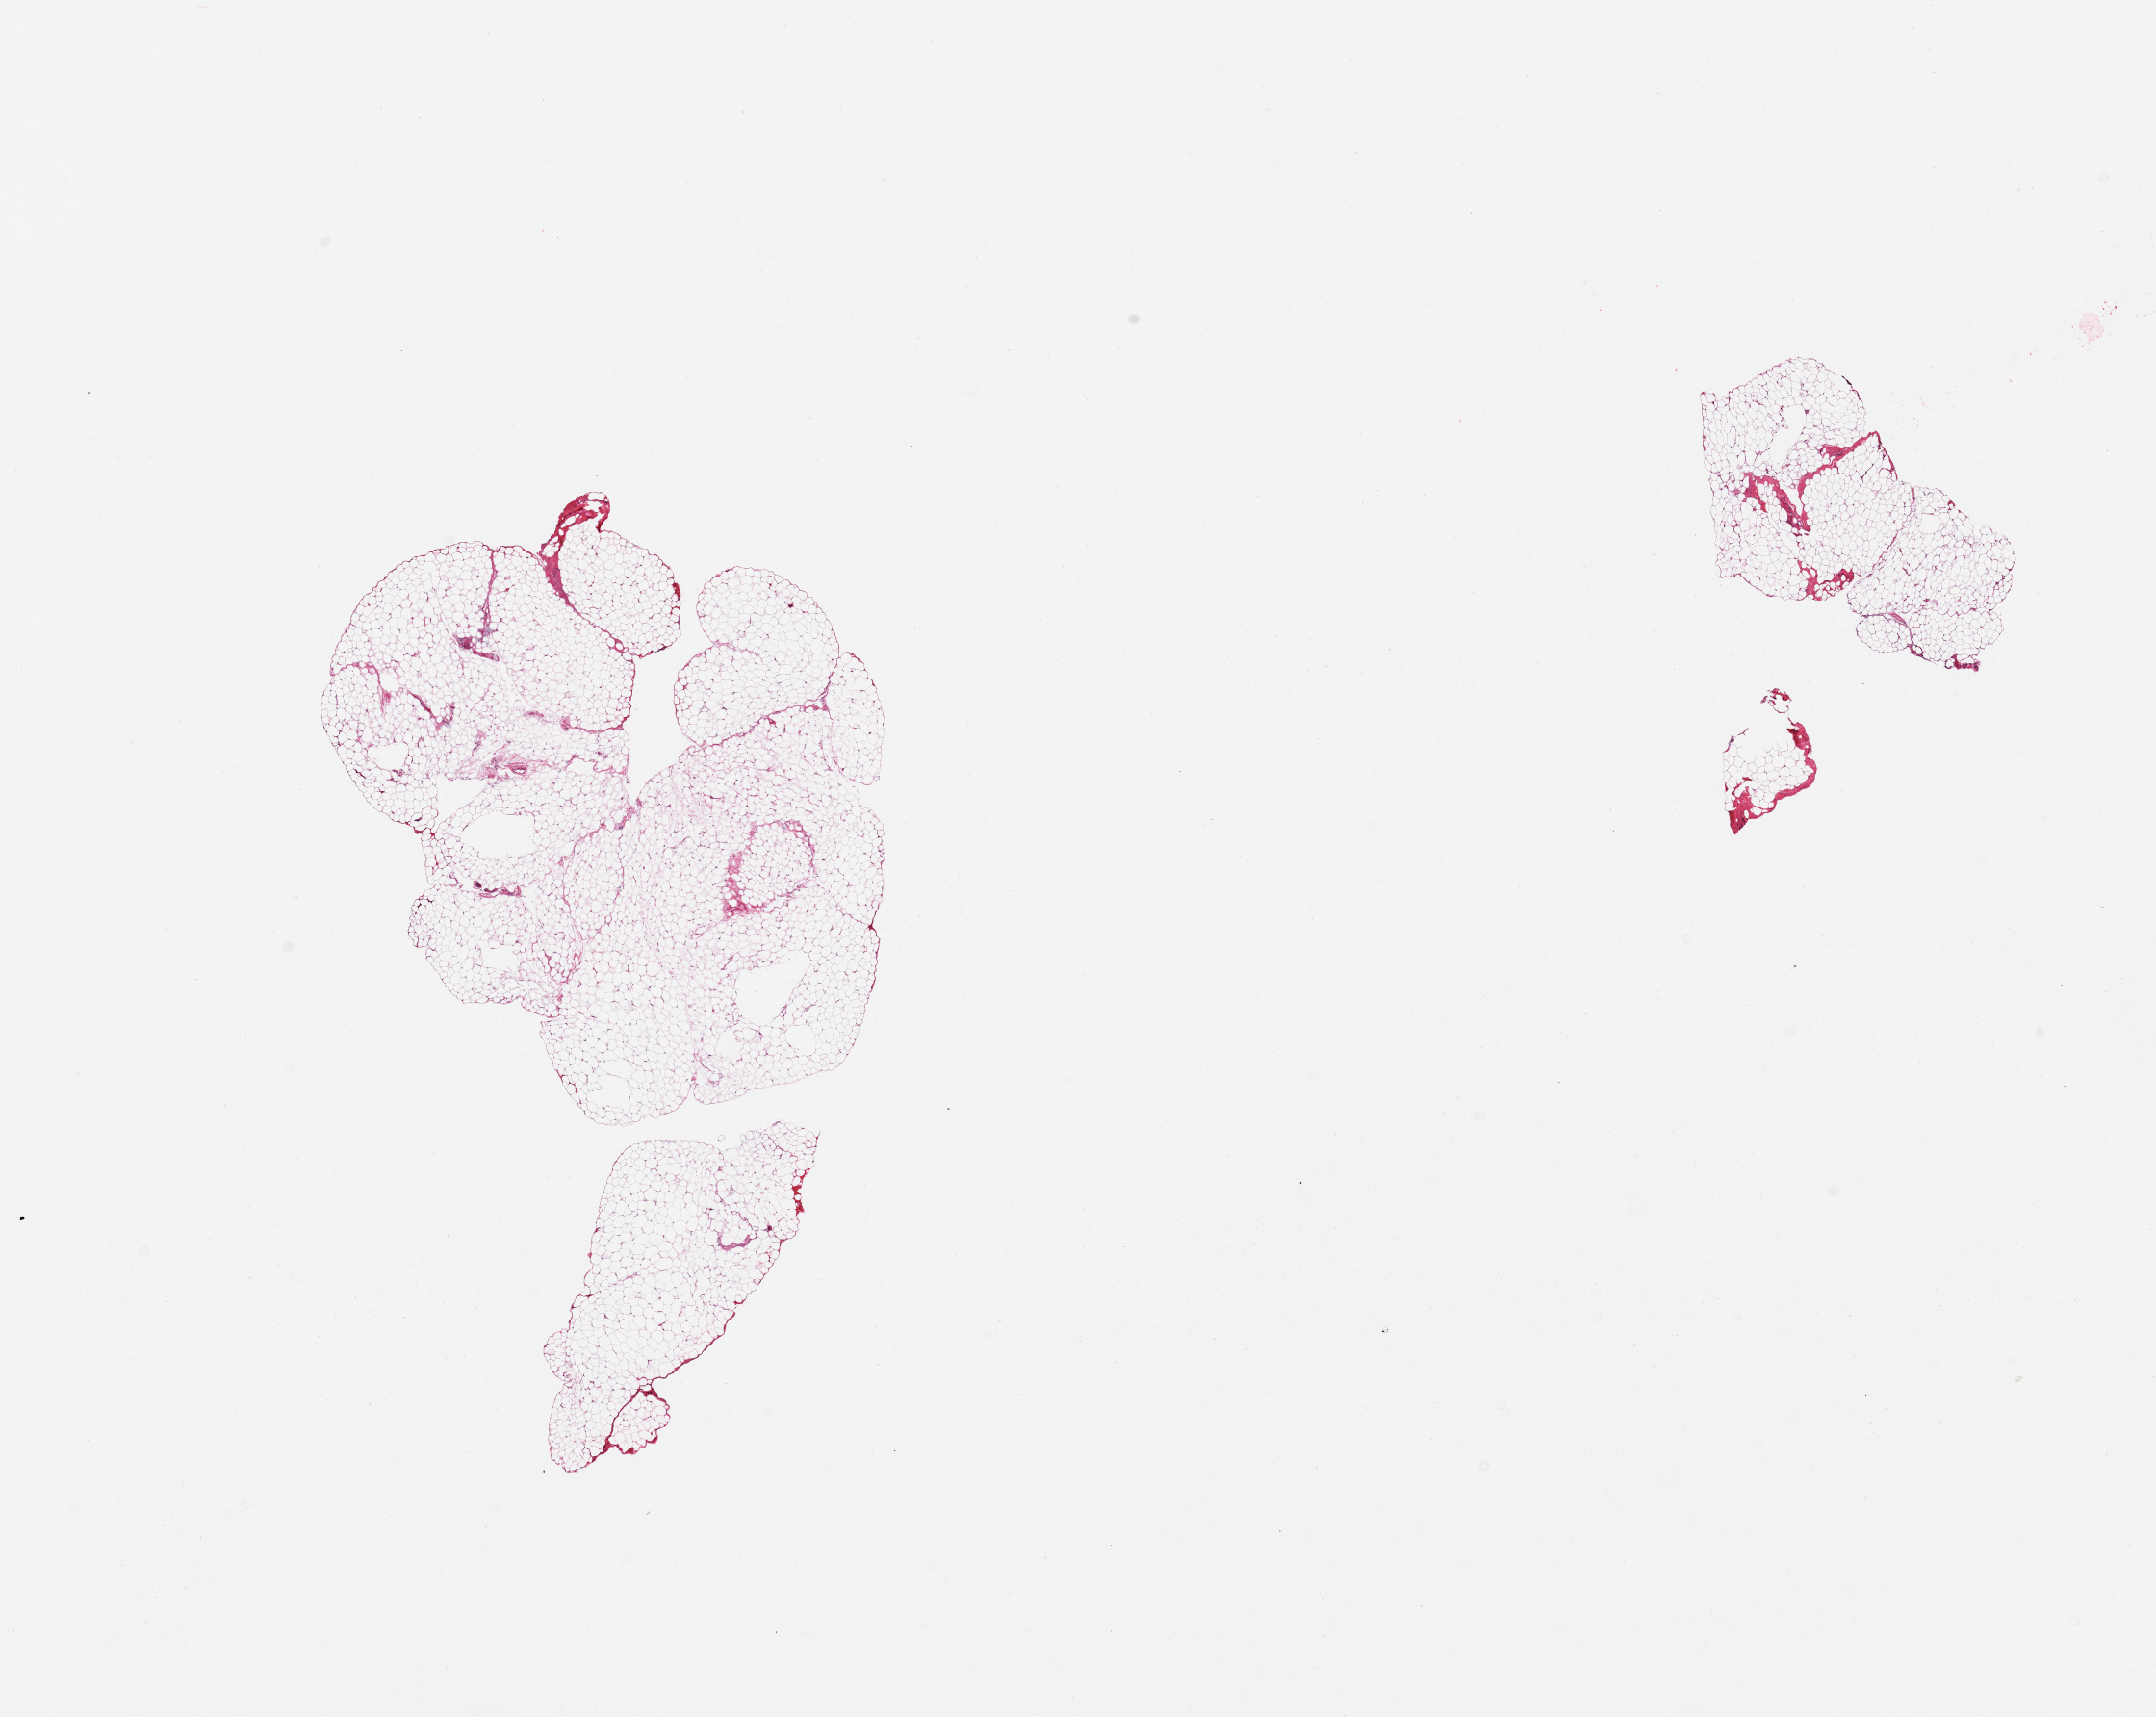
Whole-slide image, H&E stain, whole scanned area (about 17.7 x 14.1 mm) shown as a low-resolution overview; PAXgene-fixed paraffin-embedded (PFPE) section; section of omentum (target tissue); donor tissue sample. Donor sex: female.
Review note (as recorded): 1 + 2 small pieces; low fibrous content.